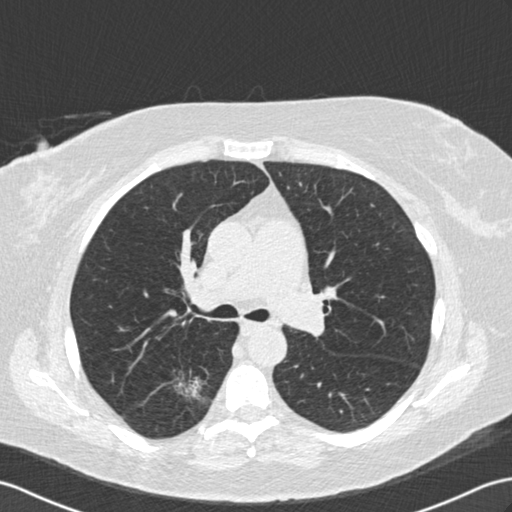
Axial slice from a low-dose chest CT screening exam; second annual screen; lung window (W 1500 / L -600 HU); 2 mm slice thickness; 120 kVp; slice 57 of 154 in the series. Female participant, aged 65 years at enrolment. Former smoker at enrolment.
Lesion marked by an expert reader, bounding box [x1, y1, x2, y2] px = [157, 357, 215, 415]. The exam's reader record, not a measurement of the box and not confirmed to be the same lesion: non-calcified nodule or mass ≥4 mm, right lower lobe, 18 × 16 mm, spiculated (stellate) margins, soft tissue attenuation, pre-existing on the prior screen: yes; interval growth: yes. Lung cancer was diagnosed 239 days after this screen: adenocarcinoma, NOS, right lower lobe, moderately differentiated (G2), stage IA (AJCC 6th edition), 25 mm at pathology.